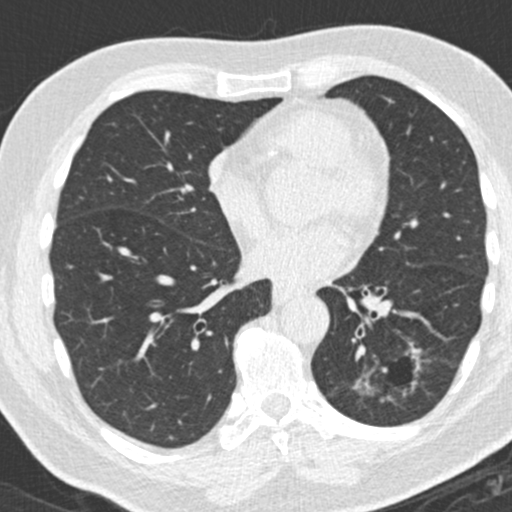
Axial slice from a low-dose chest CT screening exam. Third screening round (two years after baseline). Lung window (W 1500 / L -600 HU). Standard (soft-tissue) reconstruction kernel (B30f). Slice 96 of 180 in the series. Male, age 66 years at enrolment. Former smoker at enrolment.
Lesion marked by an expert reader, bounding box [x1, y1, x2, y2] px = [355, 345, 427, 429]. The exam's reader record, not a measurement of the box and not confirmed to be the same lesion: non-calcified nodule or mass ≥4 mm, left lower lobe, 31 × 24 mm, spiculated (stellate) margins, pre-existing on the prior screen: yes; interval growth: yes. Official screen result: positive, other. Participant outcome: lung cancer diagnosed 56 days after this screen — adenocarcinoma, NOS, left lower lobe, poorly differentiated (G3), stage IB (AJCC 6th edition), 38 mm at pathology.